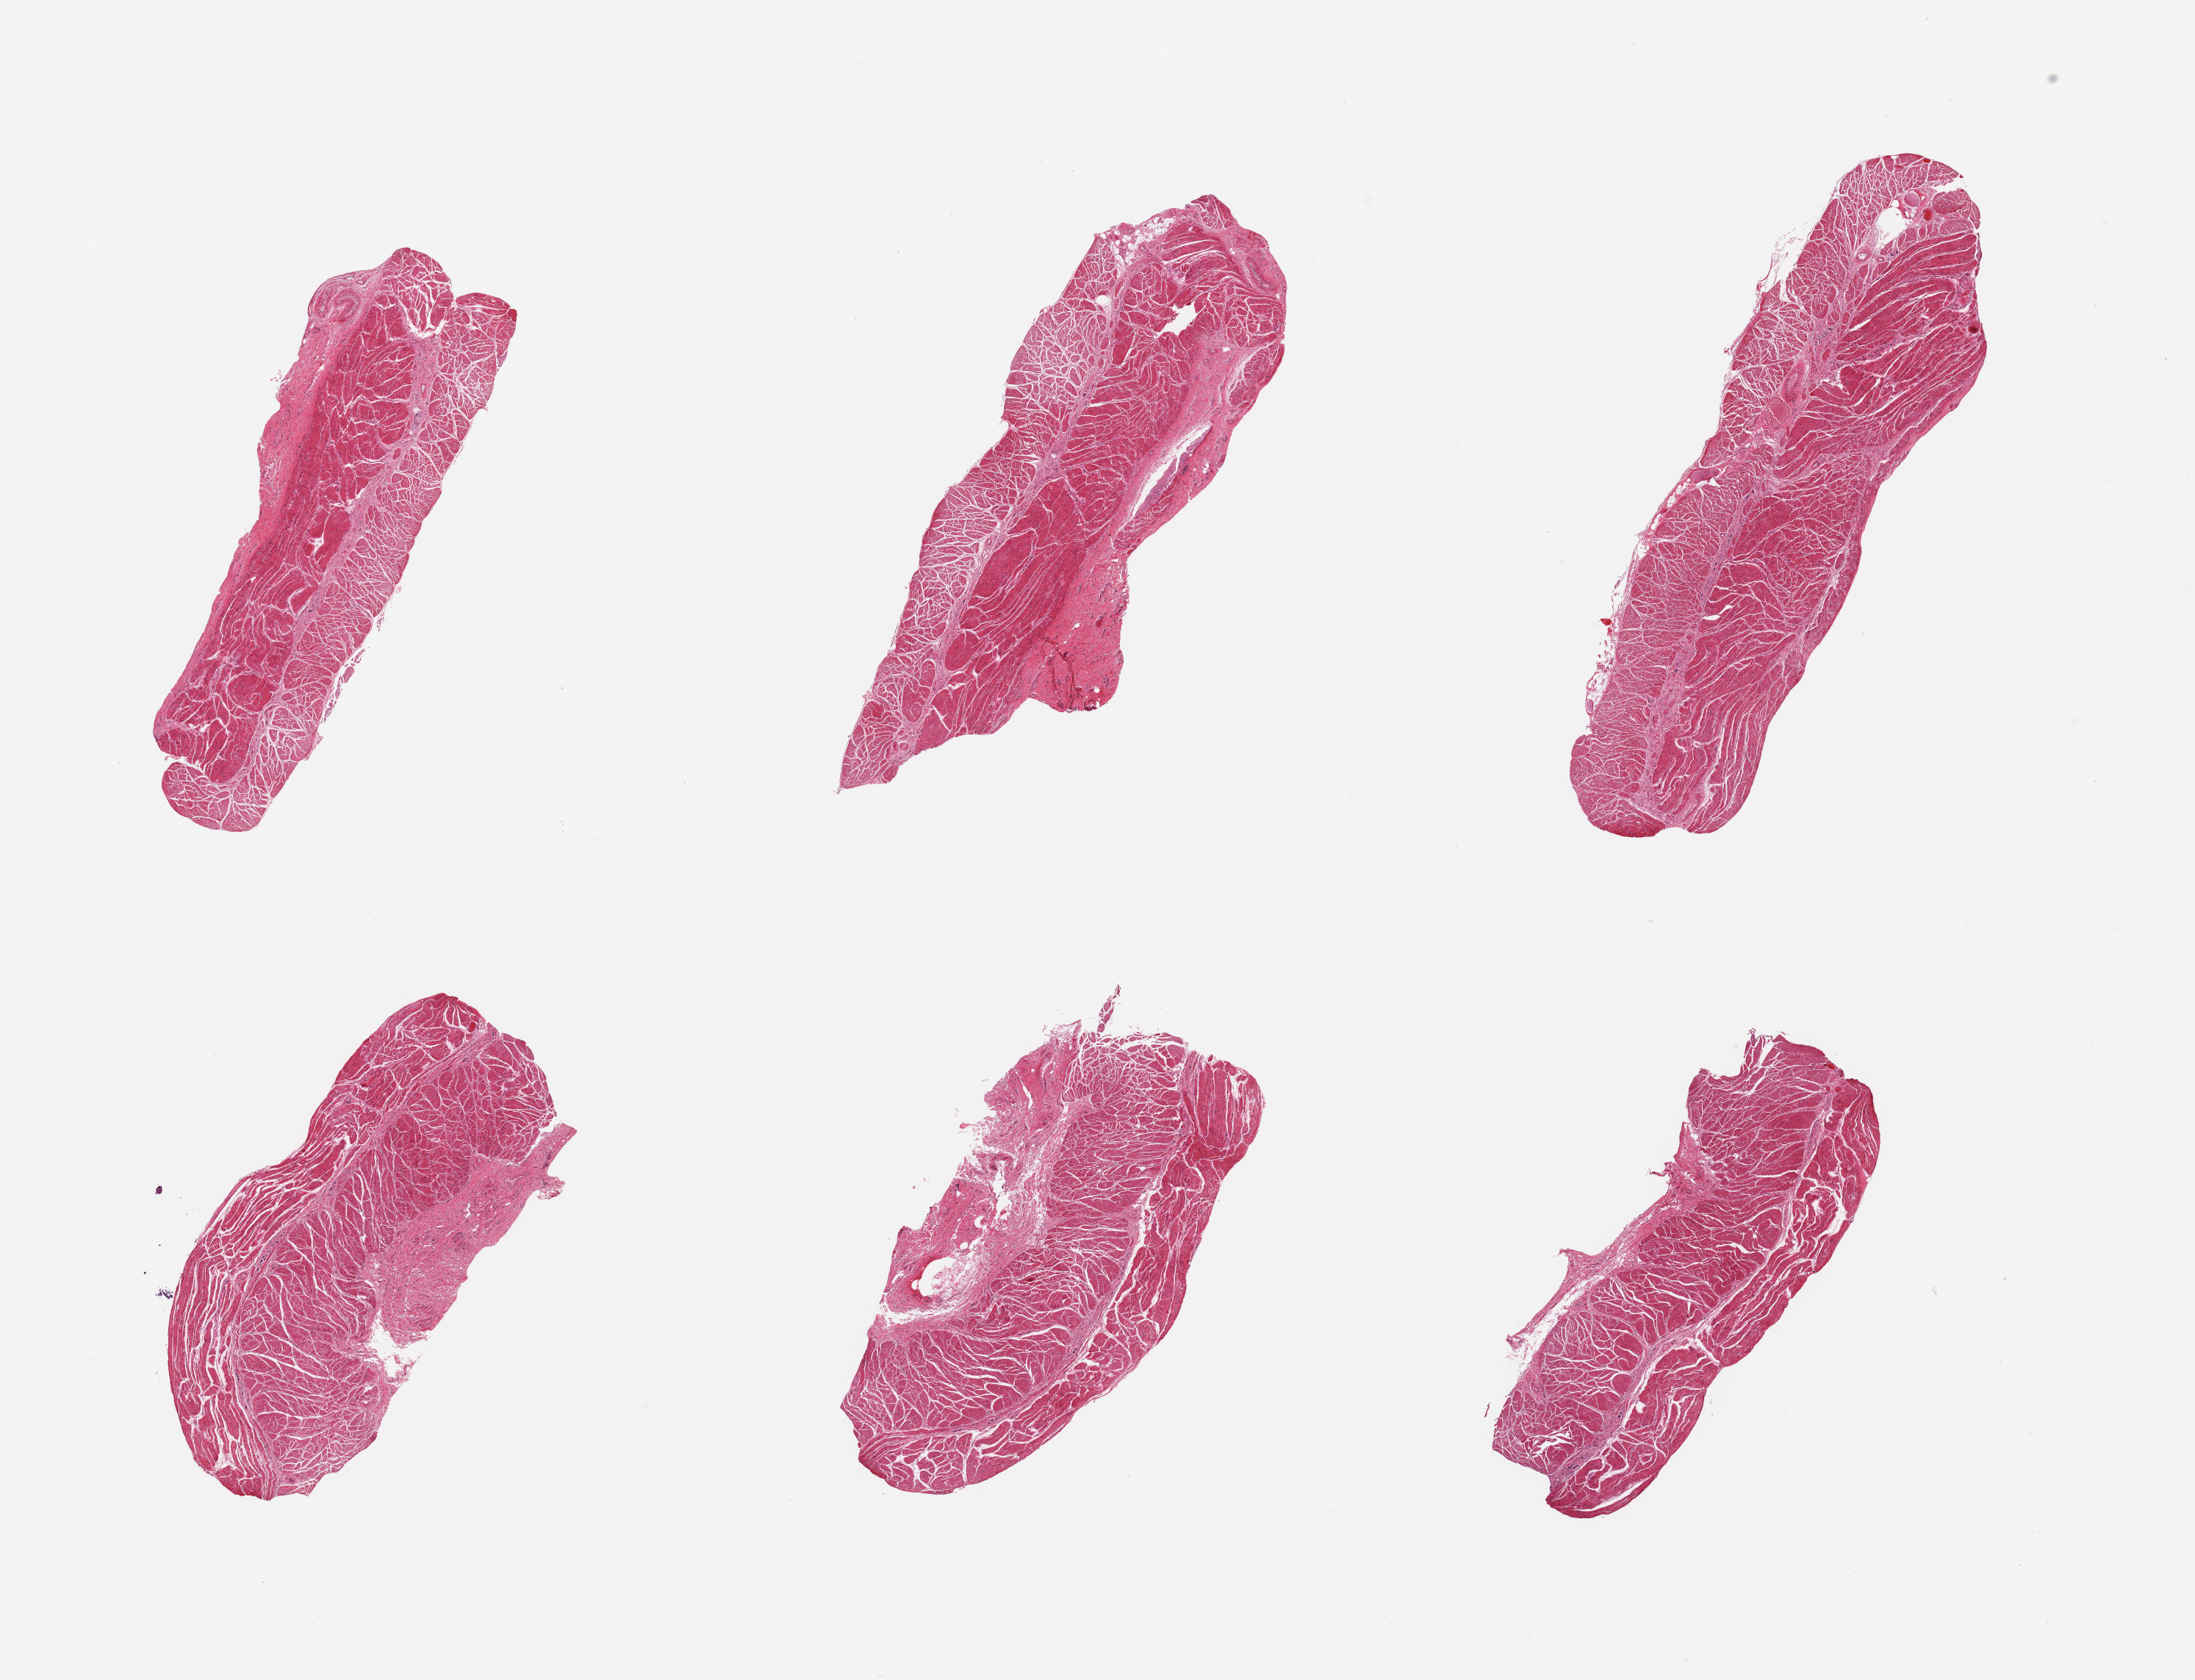
Digitized haematoxylin and eosin-stained section — low-resolution overview of the scanned area, about 23.6 x 18.1 mm (slide scanned at 20x), PAXgene-fixed paraffin-embedded (PFPE) section, target tissue: esophageal muscle, donor tissue sample. Male donor.
Review note (as recorded): 6 pieces; muscularis, well trimmed.